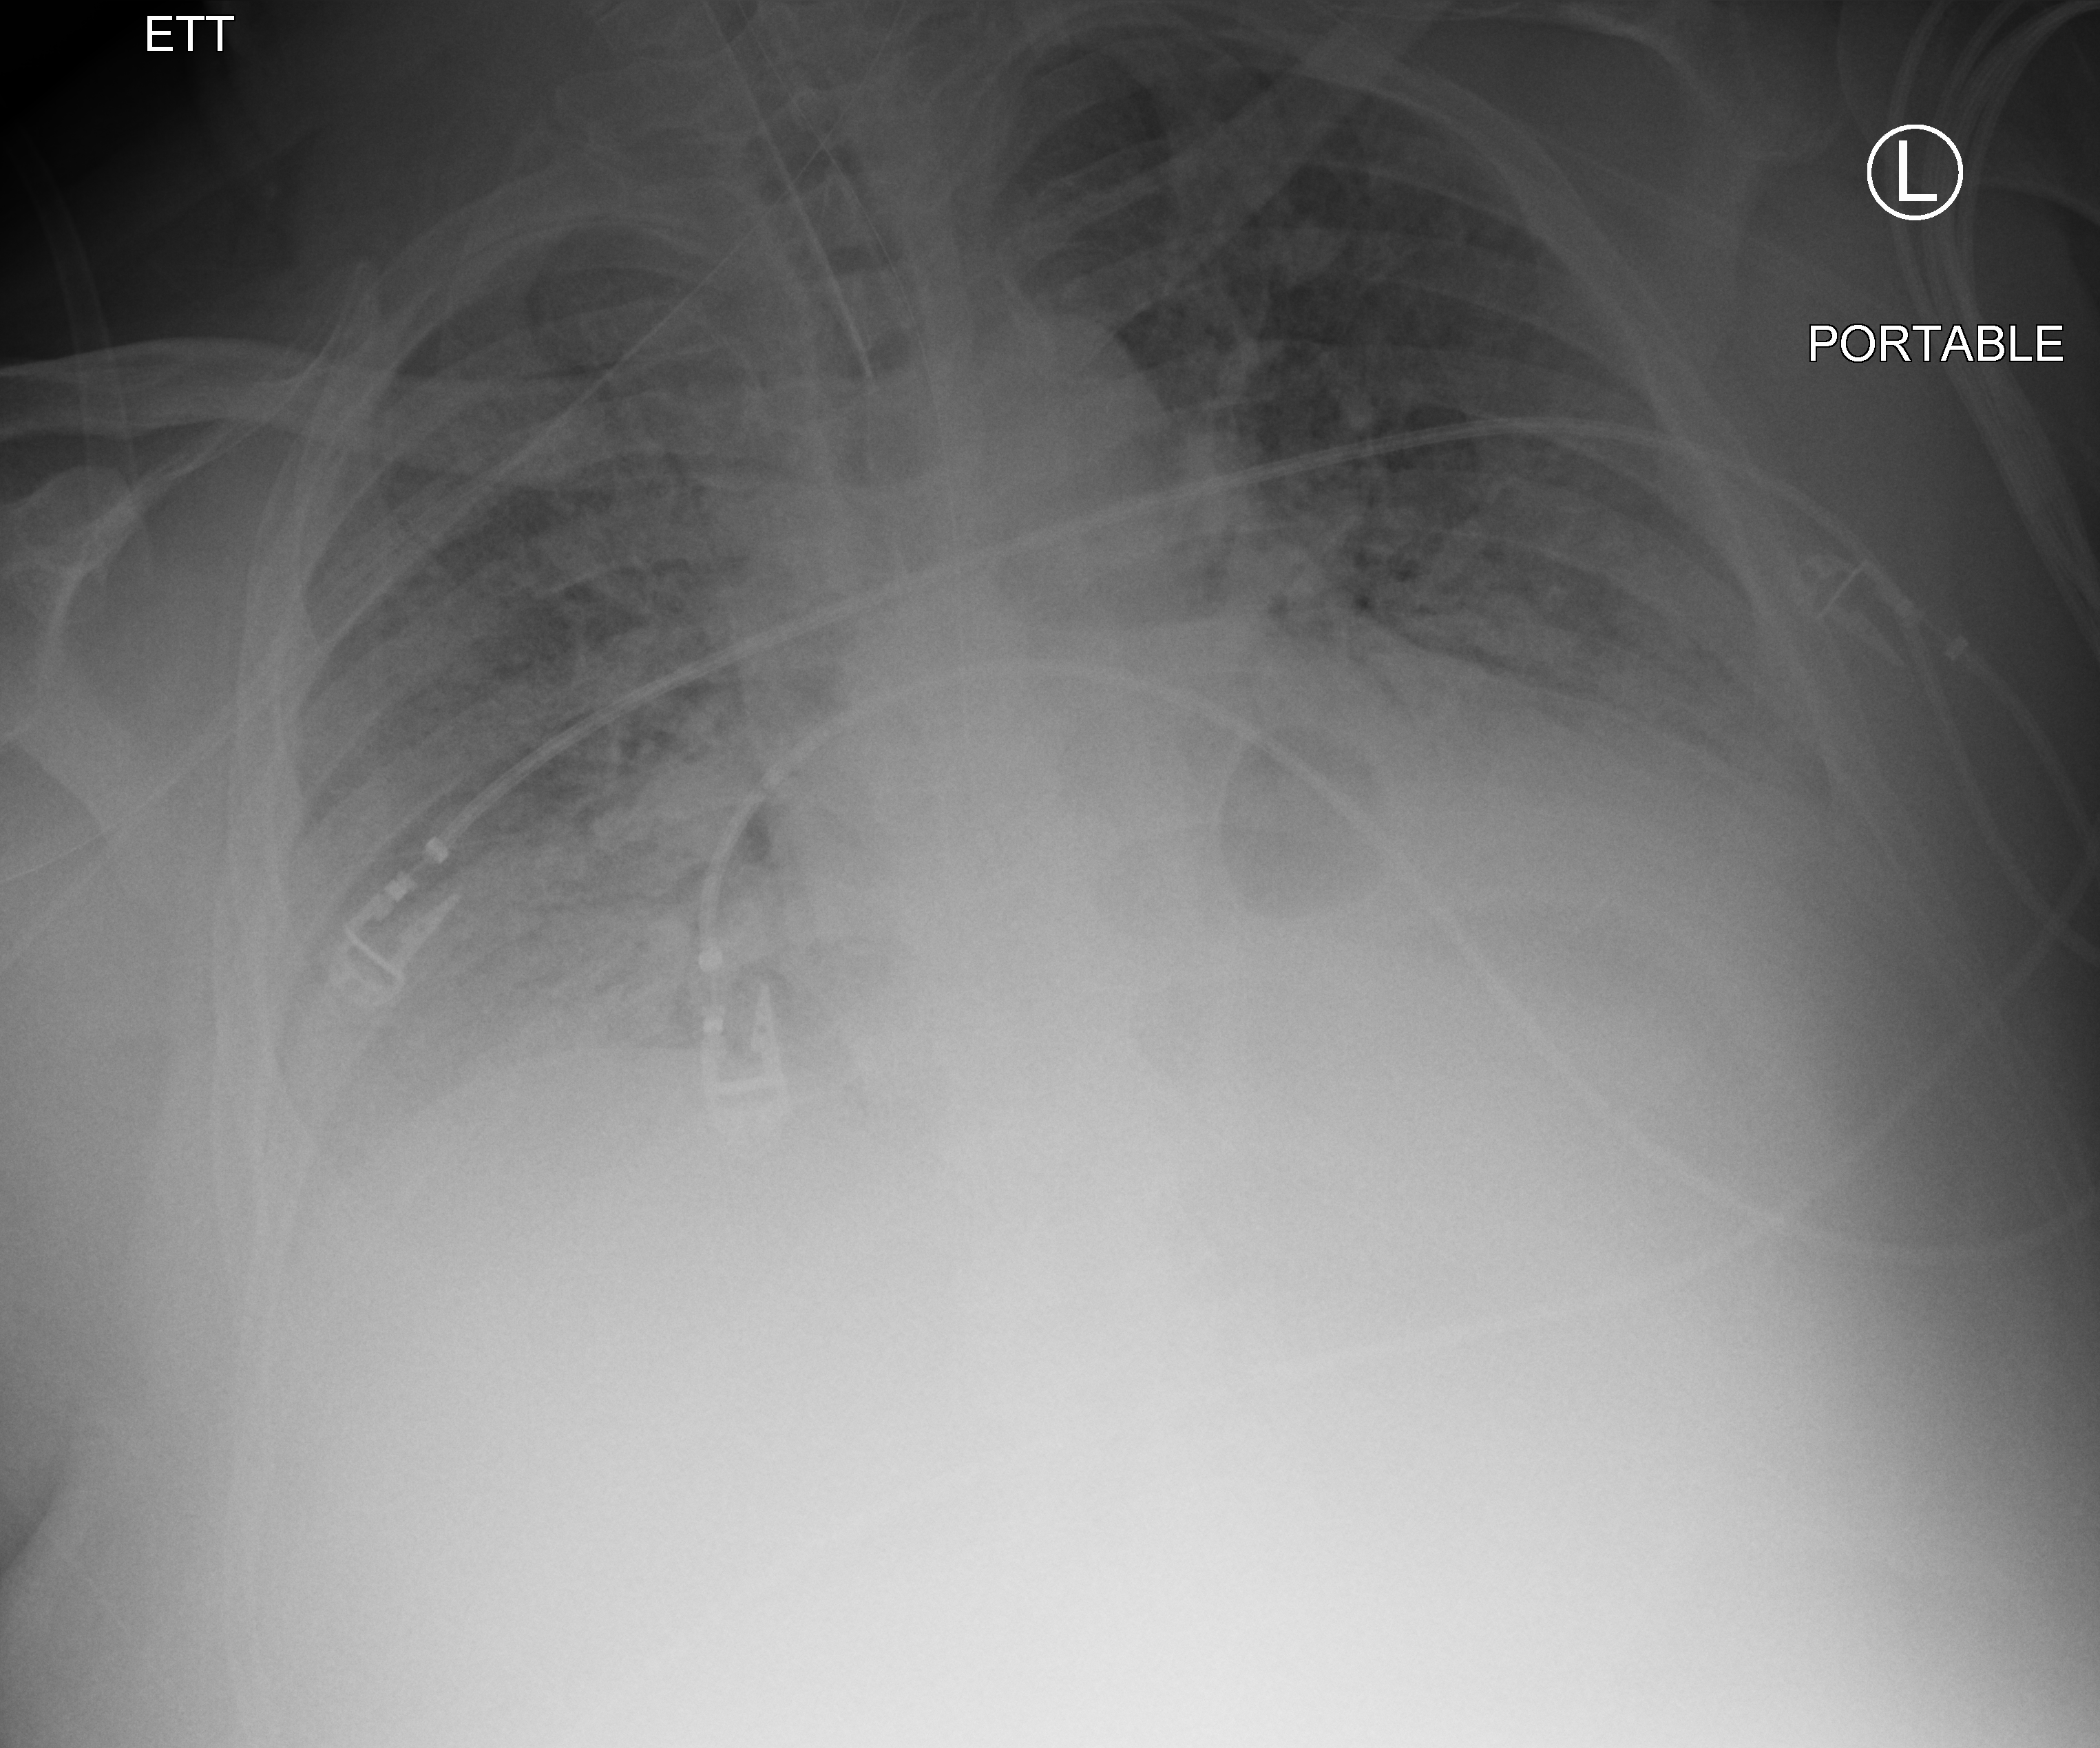
Portable chest radiograph, anteroposterior (AP) projection. Adult patient hospitalised with COVID-19, age 18–59 years.
From the hospital-stay record, not from the radiograph (when in the stay this image was taken is not recorded): admitted to intensive care during this hospital stay: yes; mechanically ventilated during this hospital stay: yes.